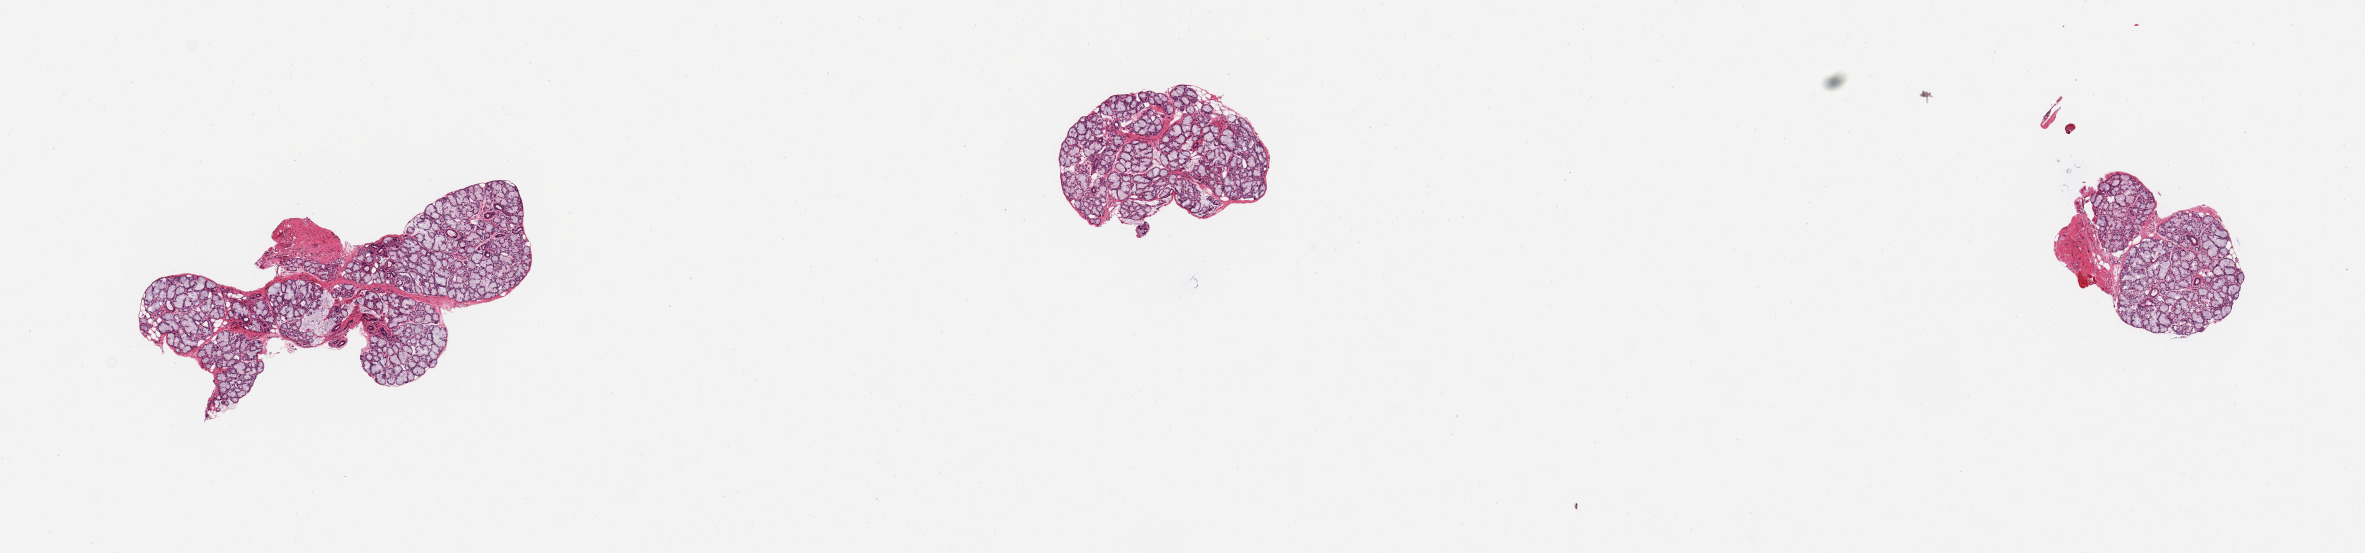
H&E whole-slide image, brightfield — a low-resolution overview of the entire scanned area, about 18.7 x 4.4 mm. PAXgene-fixed paraffin-embedded (PFPE) section. Sampled site (target tissue): minor salivary gland. Tissue donor sample. Donor sex: male.
Review note (as recorded): 3 pieces; essentially well trimmed although two pieces contain small fragments of fibrous tissue.